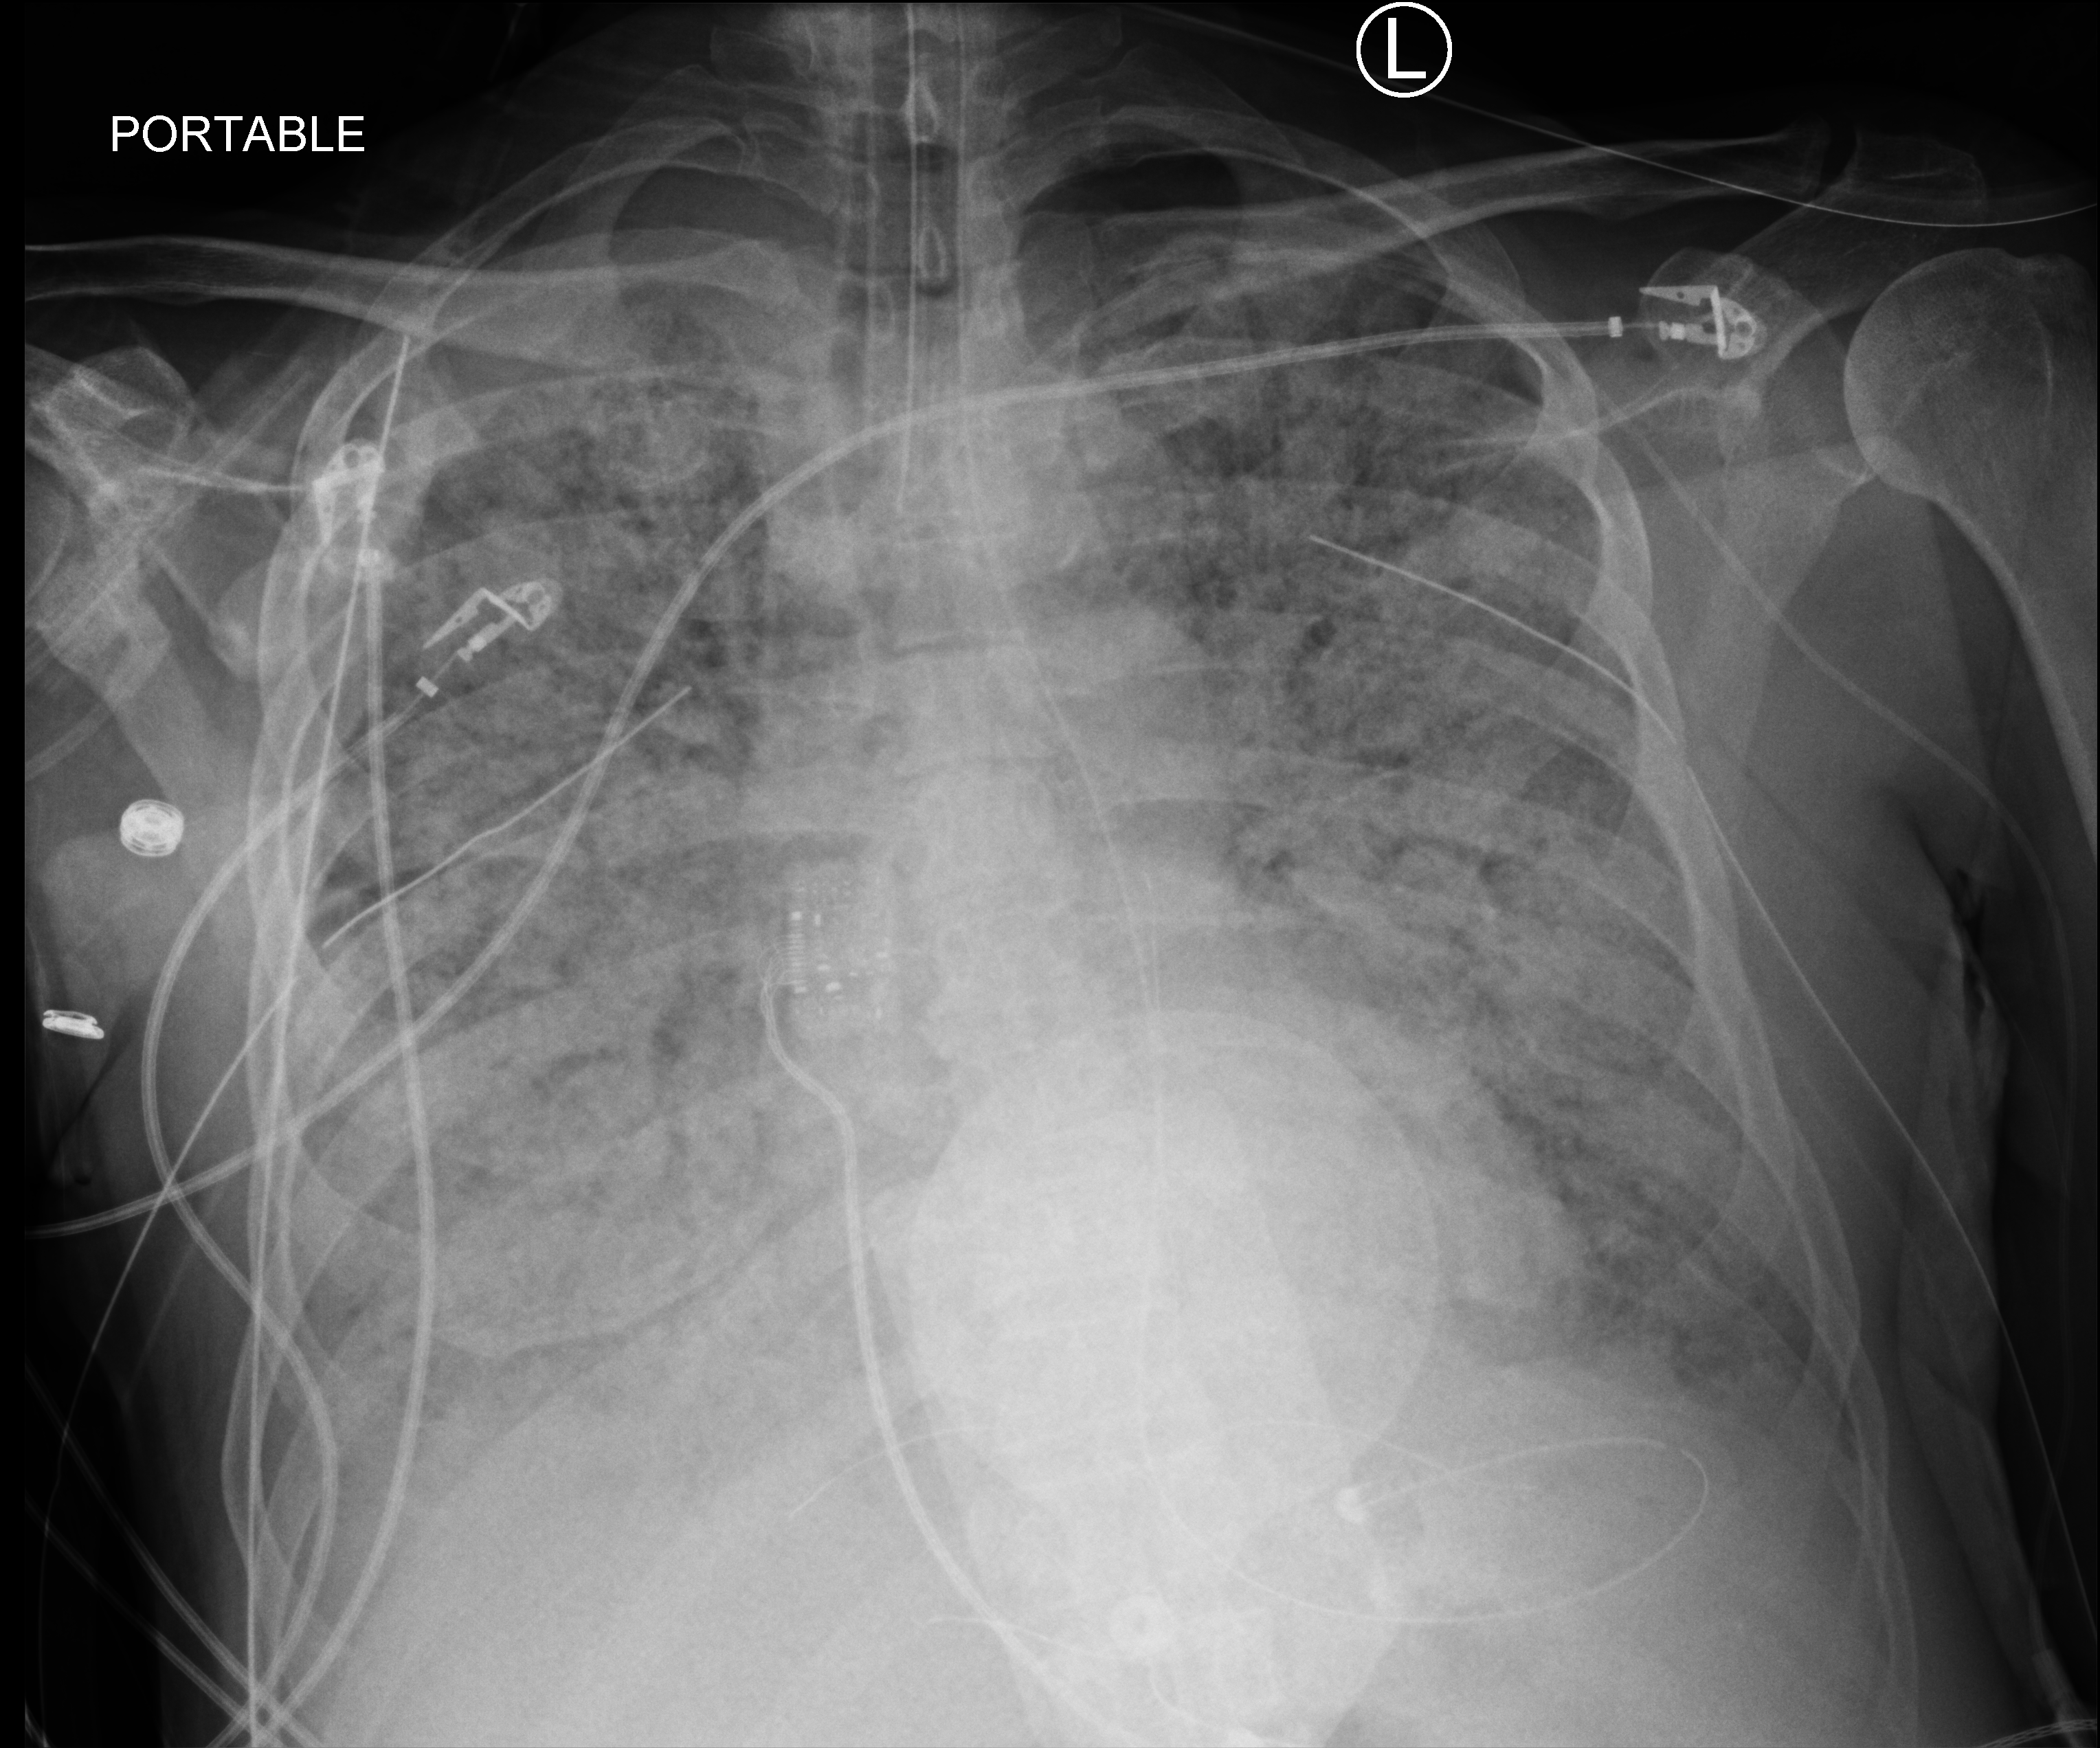
Portable chest radiograph; anteroposterior (AP) projection. Male patient hospitalised with COVID-19, age 60–74 years.
Admission-level facts for this patient (not findings on this image; timing relative to this image not recorded): mechanically ventilated during this hospital stay: yes.